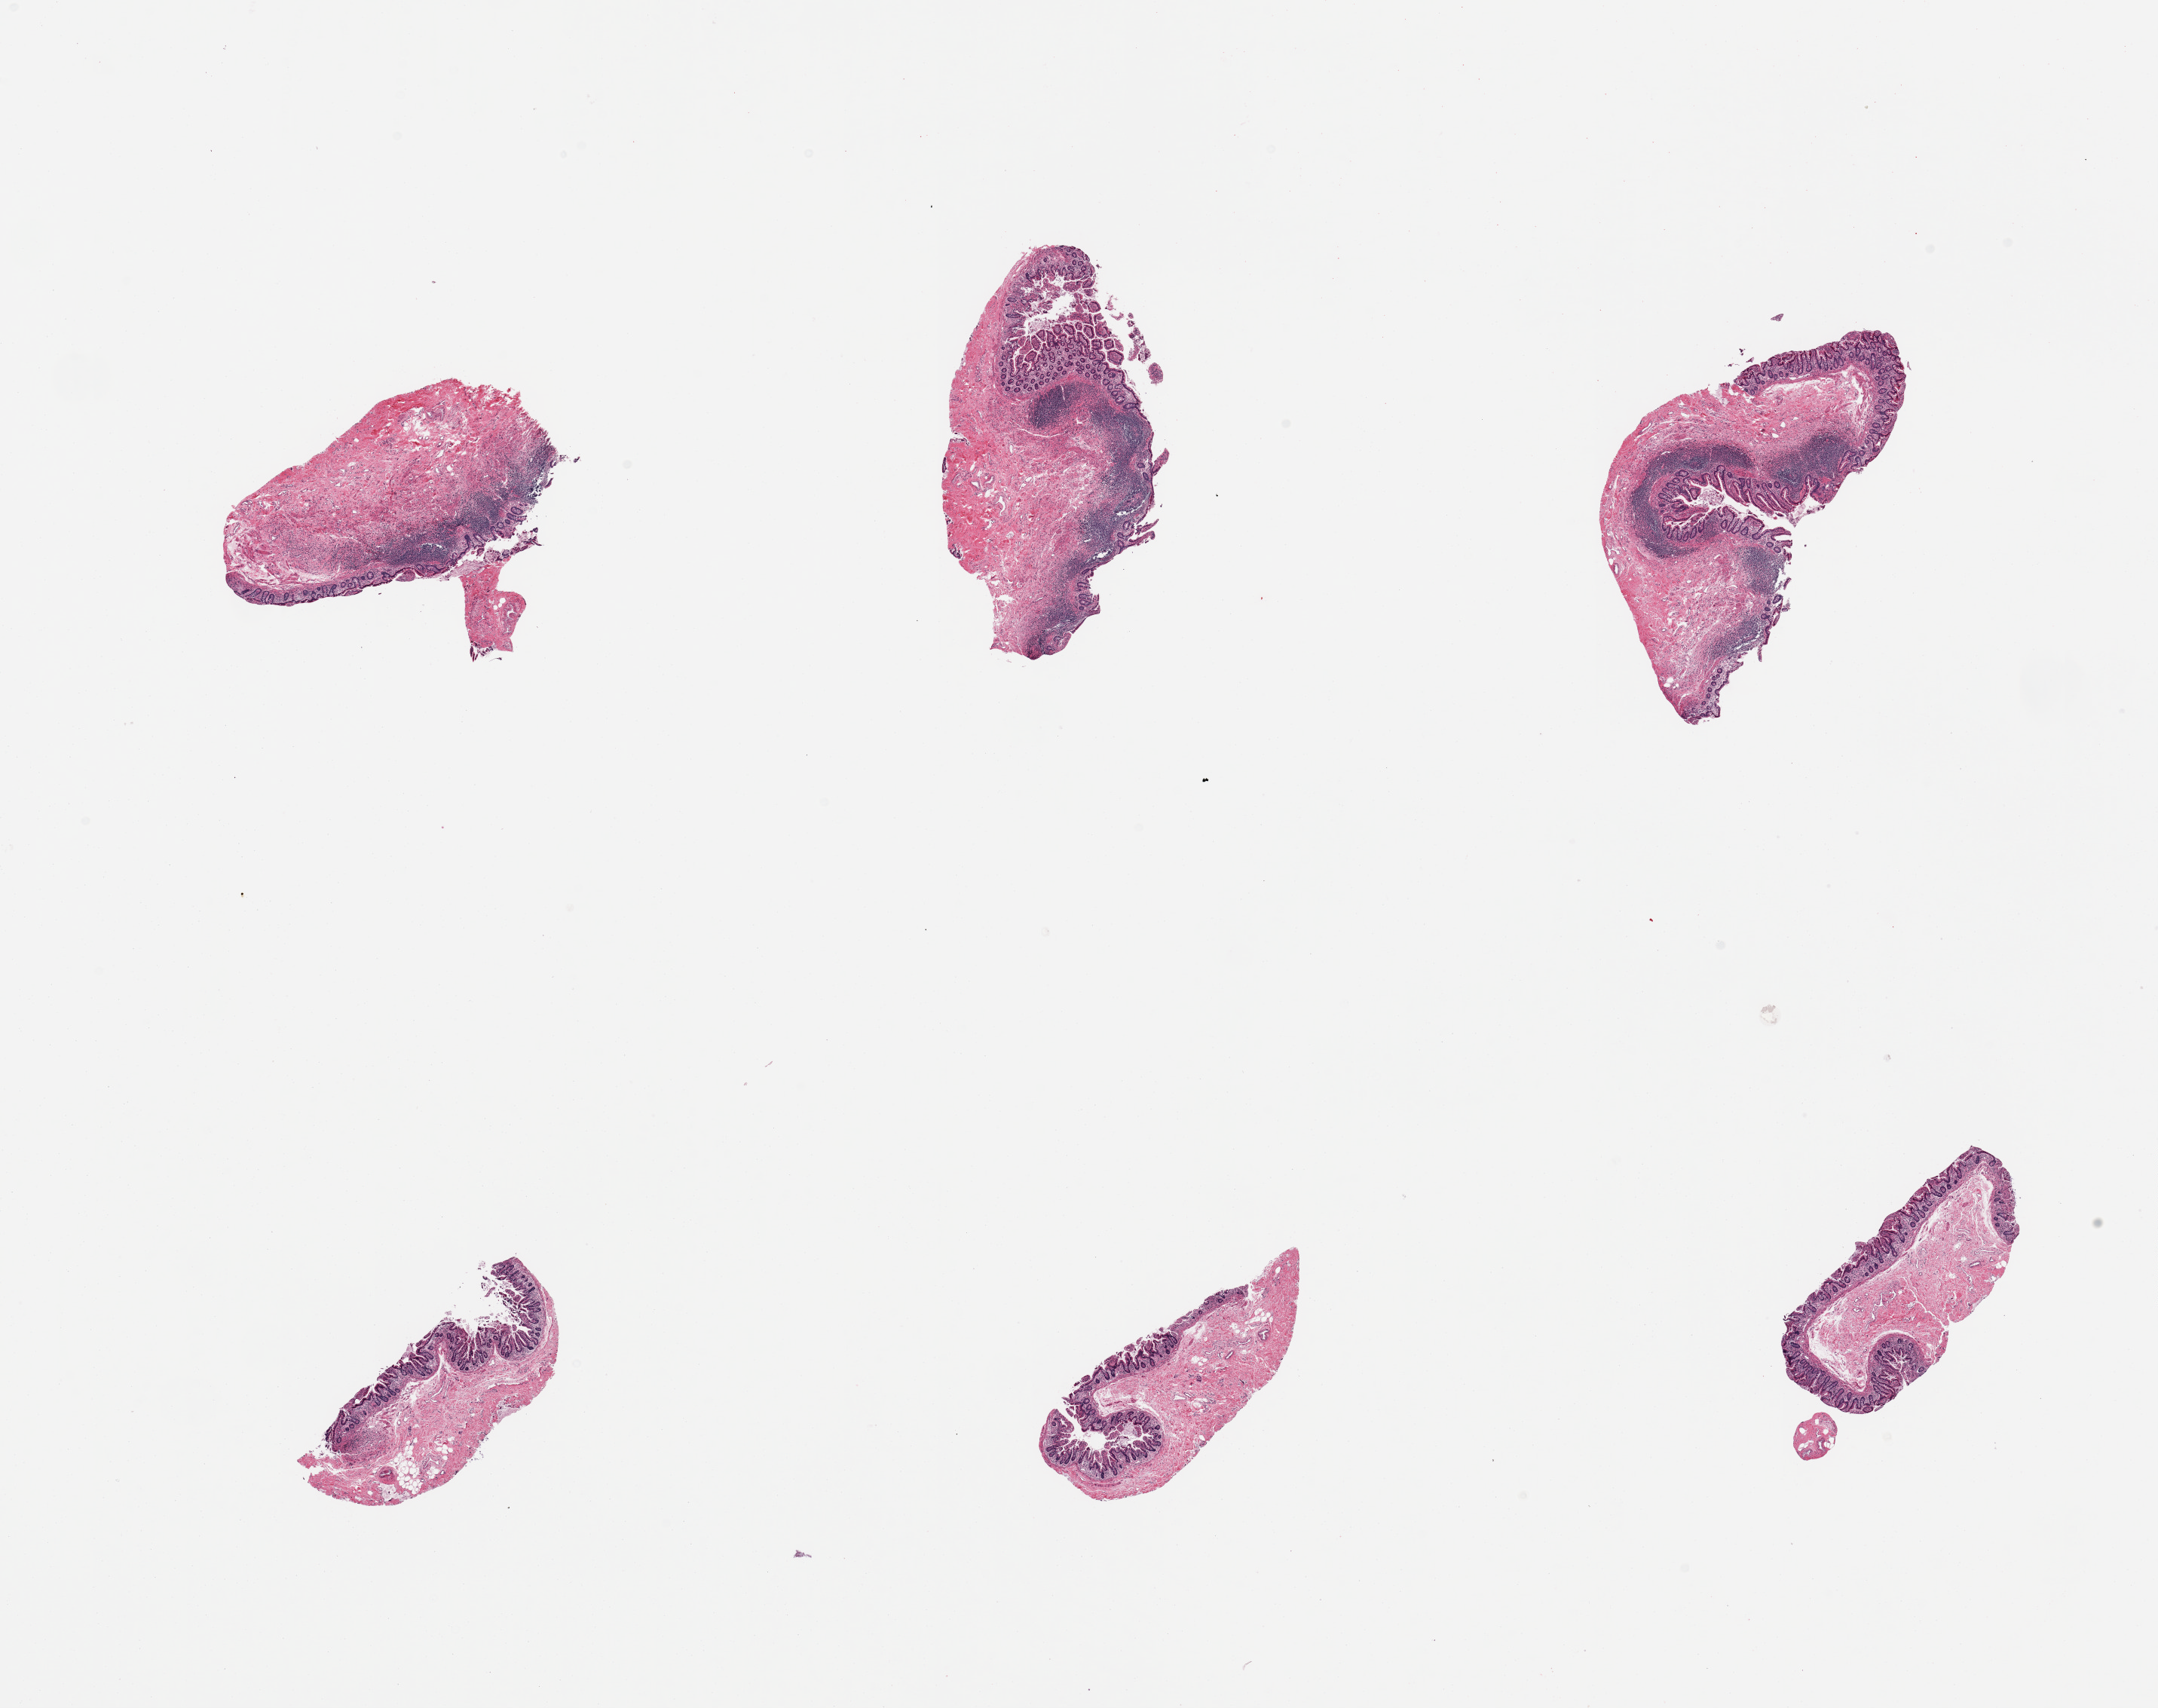
Whole-slide image, haematoxylin and eosin stain, brightfield, a low-resolution overview of the entire scanned area, about 22.6 x 17.9 mm, PAXgene-fixed, paraffin-embedded tissue, section of ileum (target tissue), donor tissue sample. Male donor.
* review note (as recorded): 6 pieces; mucosa/submucosa with adequate lymphoid tissue in 3 of 6 sections